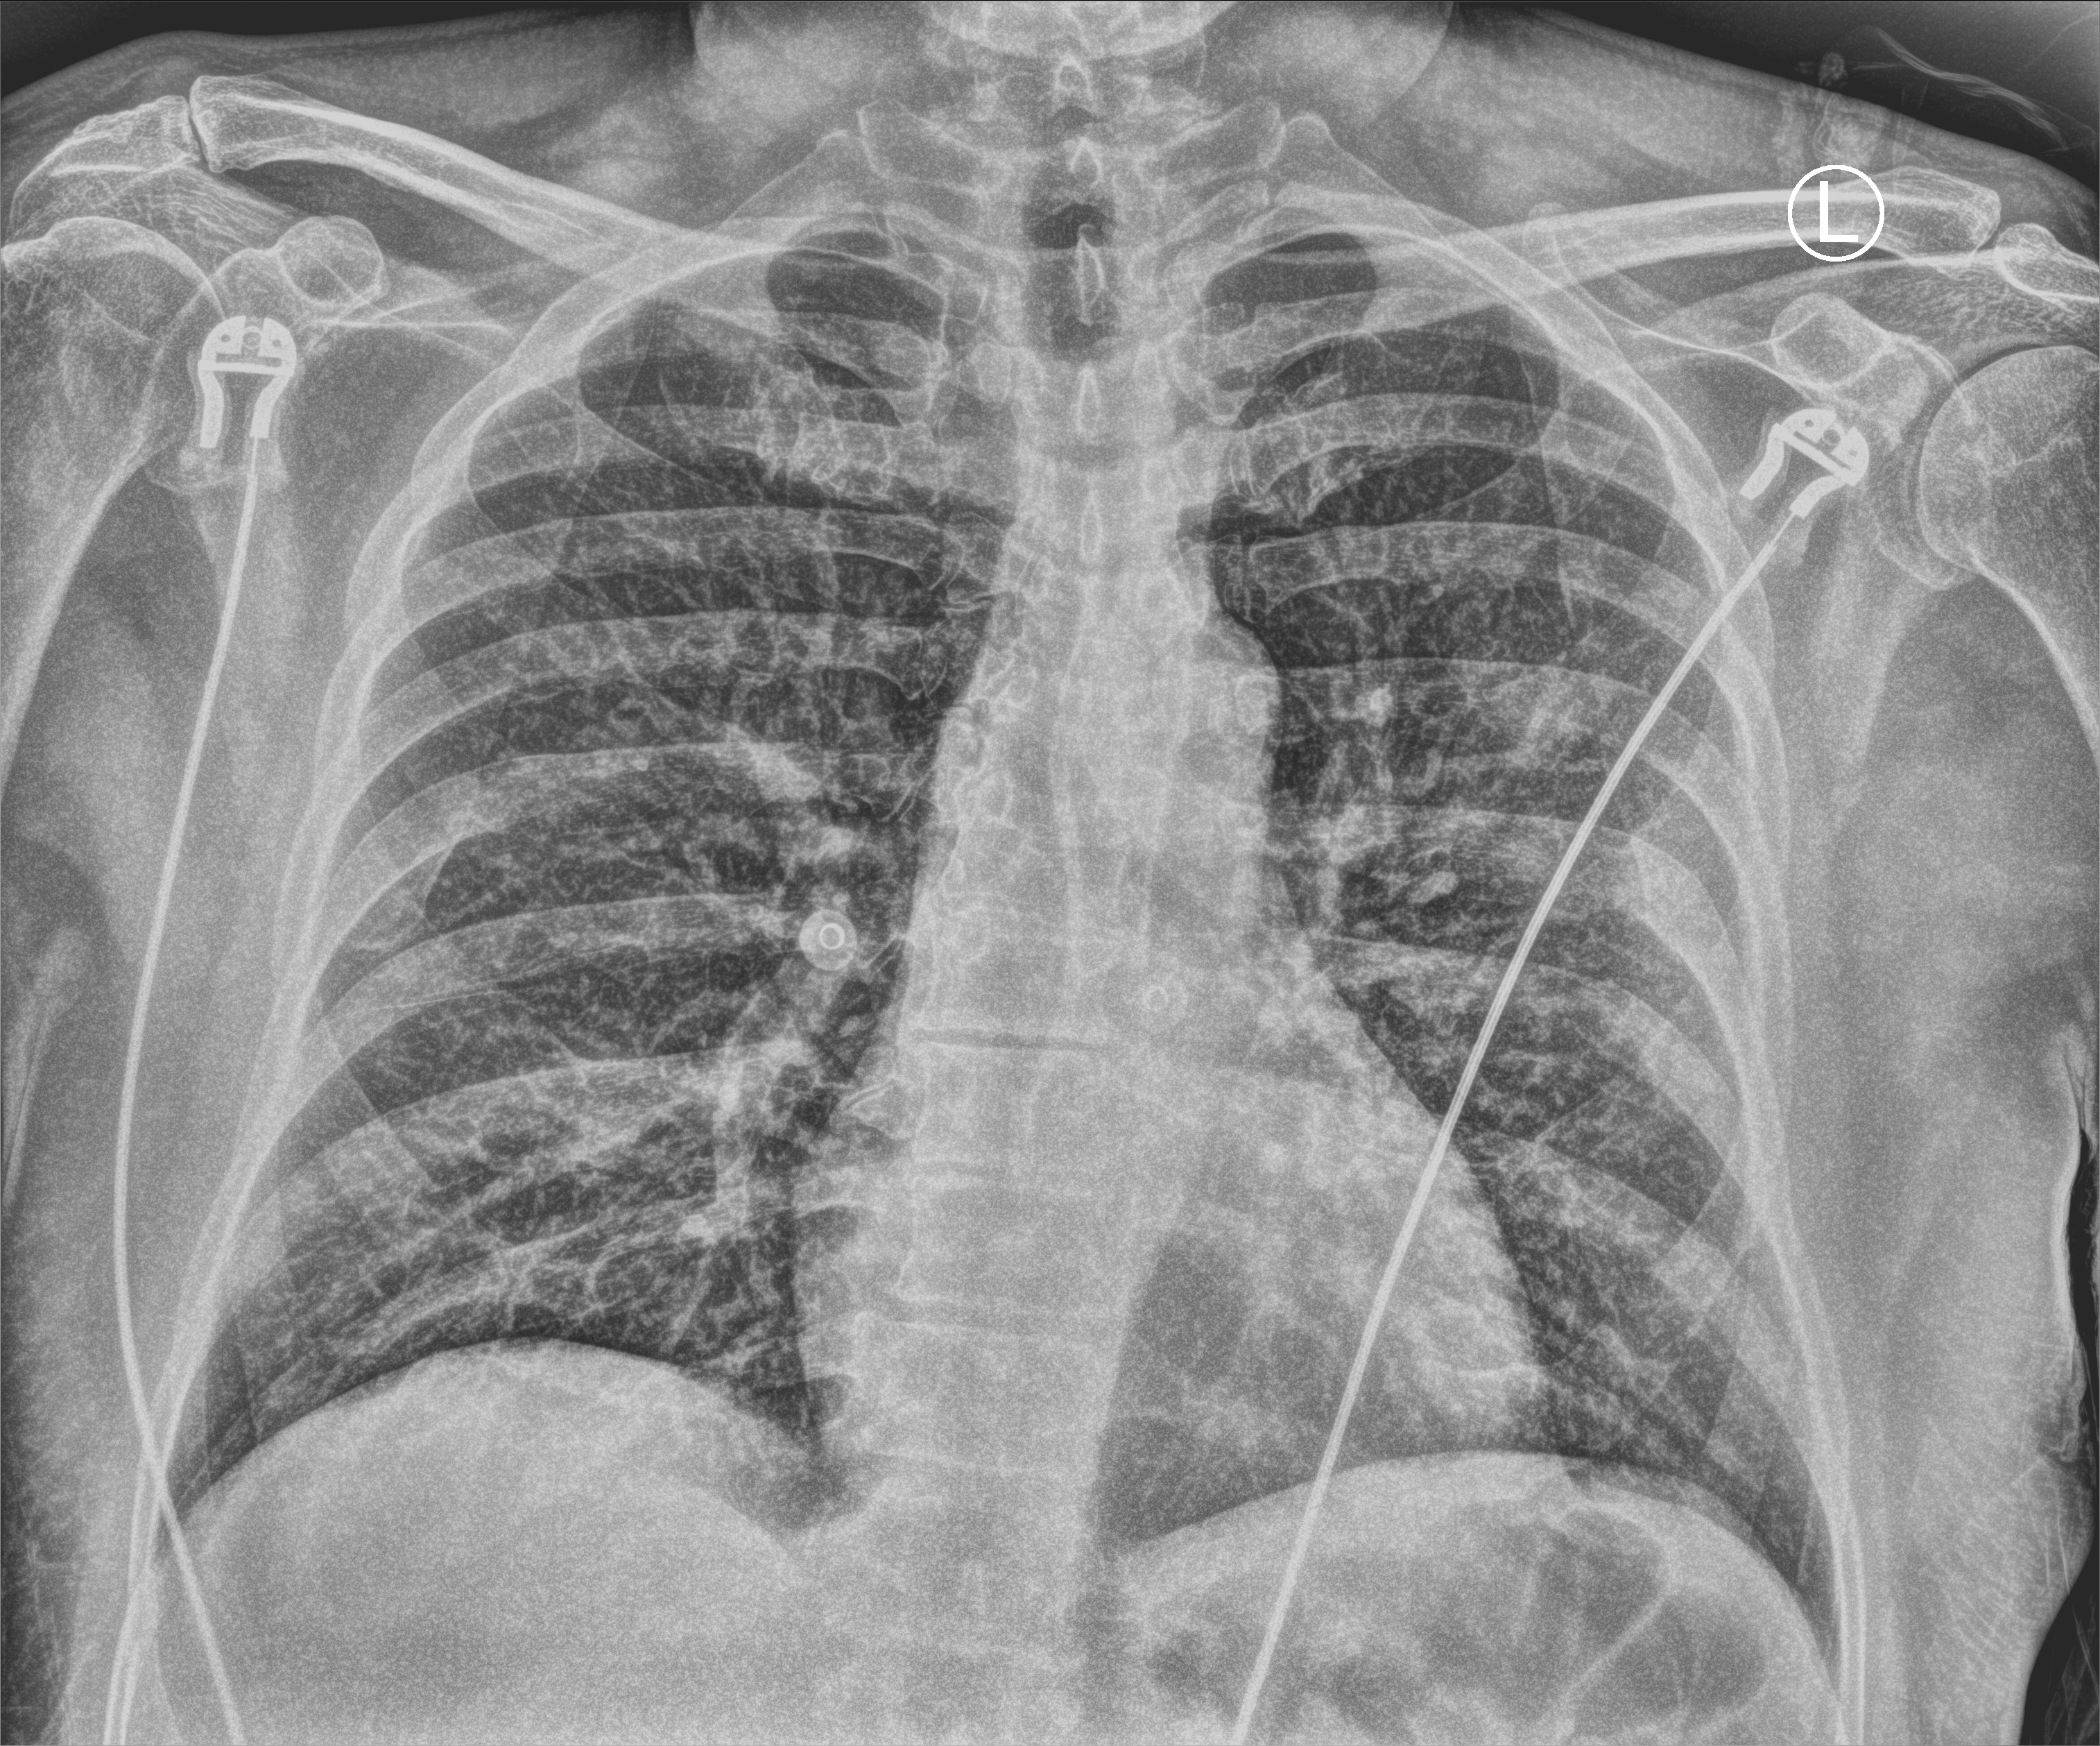
Bedside chest radiograph (computed radiography). Male patient hospitalised with COVID-19, age 60–74 years.
From the hospital-stay record, not from the radiograph (when in the stay this image was taken is not recorded):
- diabetes (admission record): no